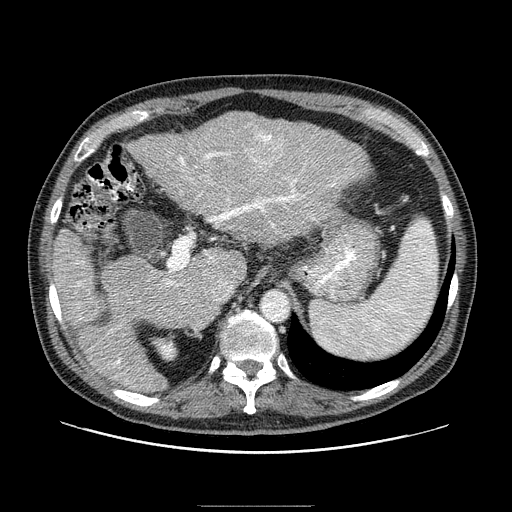
Contrast-enhanced abdominal CT (liver protocol), one axial slice; position 56 of 99 along the scan axis; one of 2 acquisitions stored at this slice position; soft-tissue window (W 400 / L 40 HU); 2.5 mm slice thickness; 512 × 512 image matrix, field of view 400 × 400 mm. From the clinical record (not read from this slice): diagnosis: hepatocellular carcinoma (patient treated with transarterial chemoembolisation; whether this scan precedes or follows treatment is not stated here); TNM stage (as recorded): Stage-II; Child-Pugh class: A; tumour size: 3.2 cm.
Structures marked on this image (semi-automatic segmentation, software-assisted and operator-edited):
- liver parenchyma outside the tumour (the mass and vessels are separate outlines, so this box may not span the whole liver): bounding box <48,112,368,388> (left, top, right, bottom; pixels)
- mass: <243,127,288,172>
- liver vessels: <77,152,339,383>